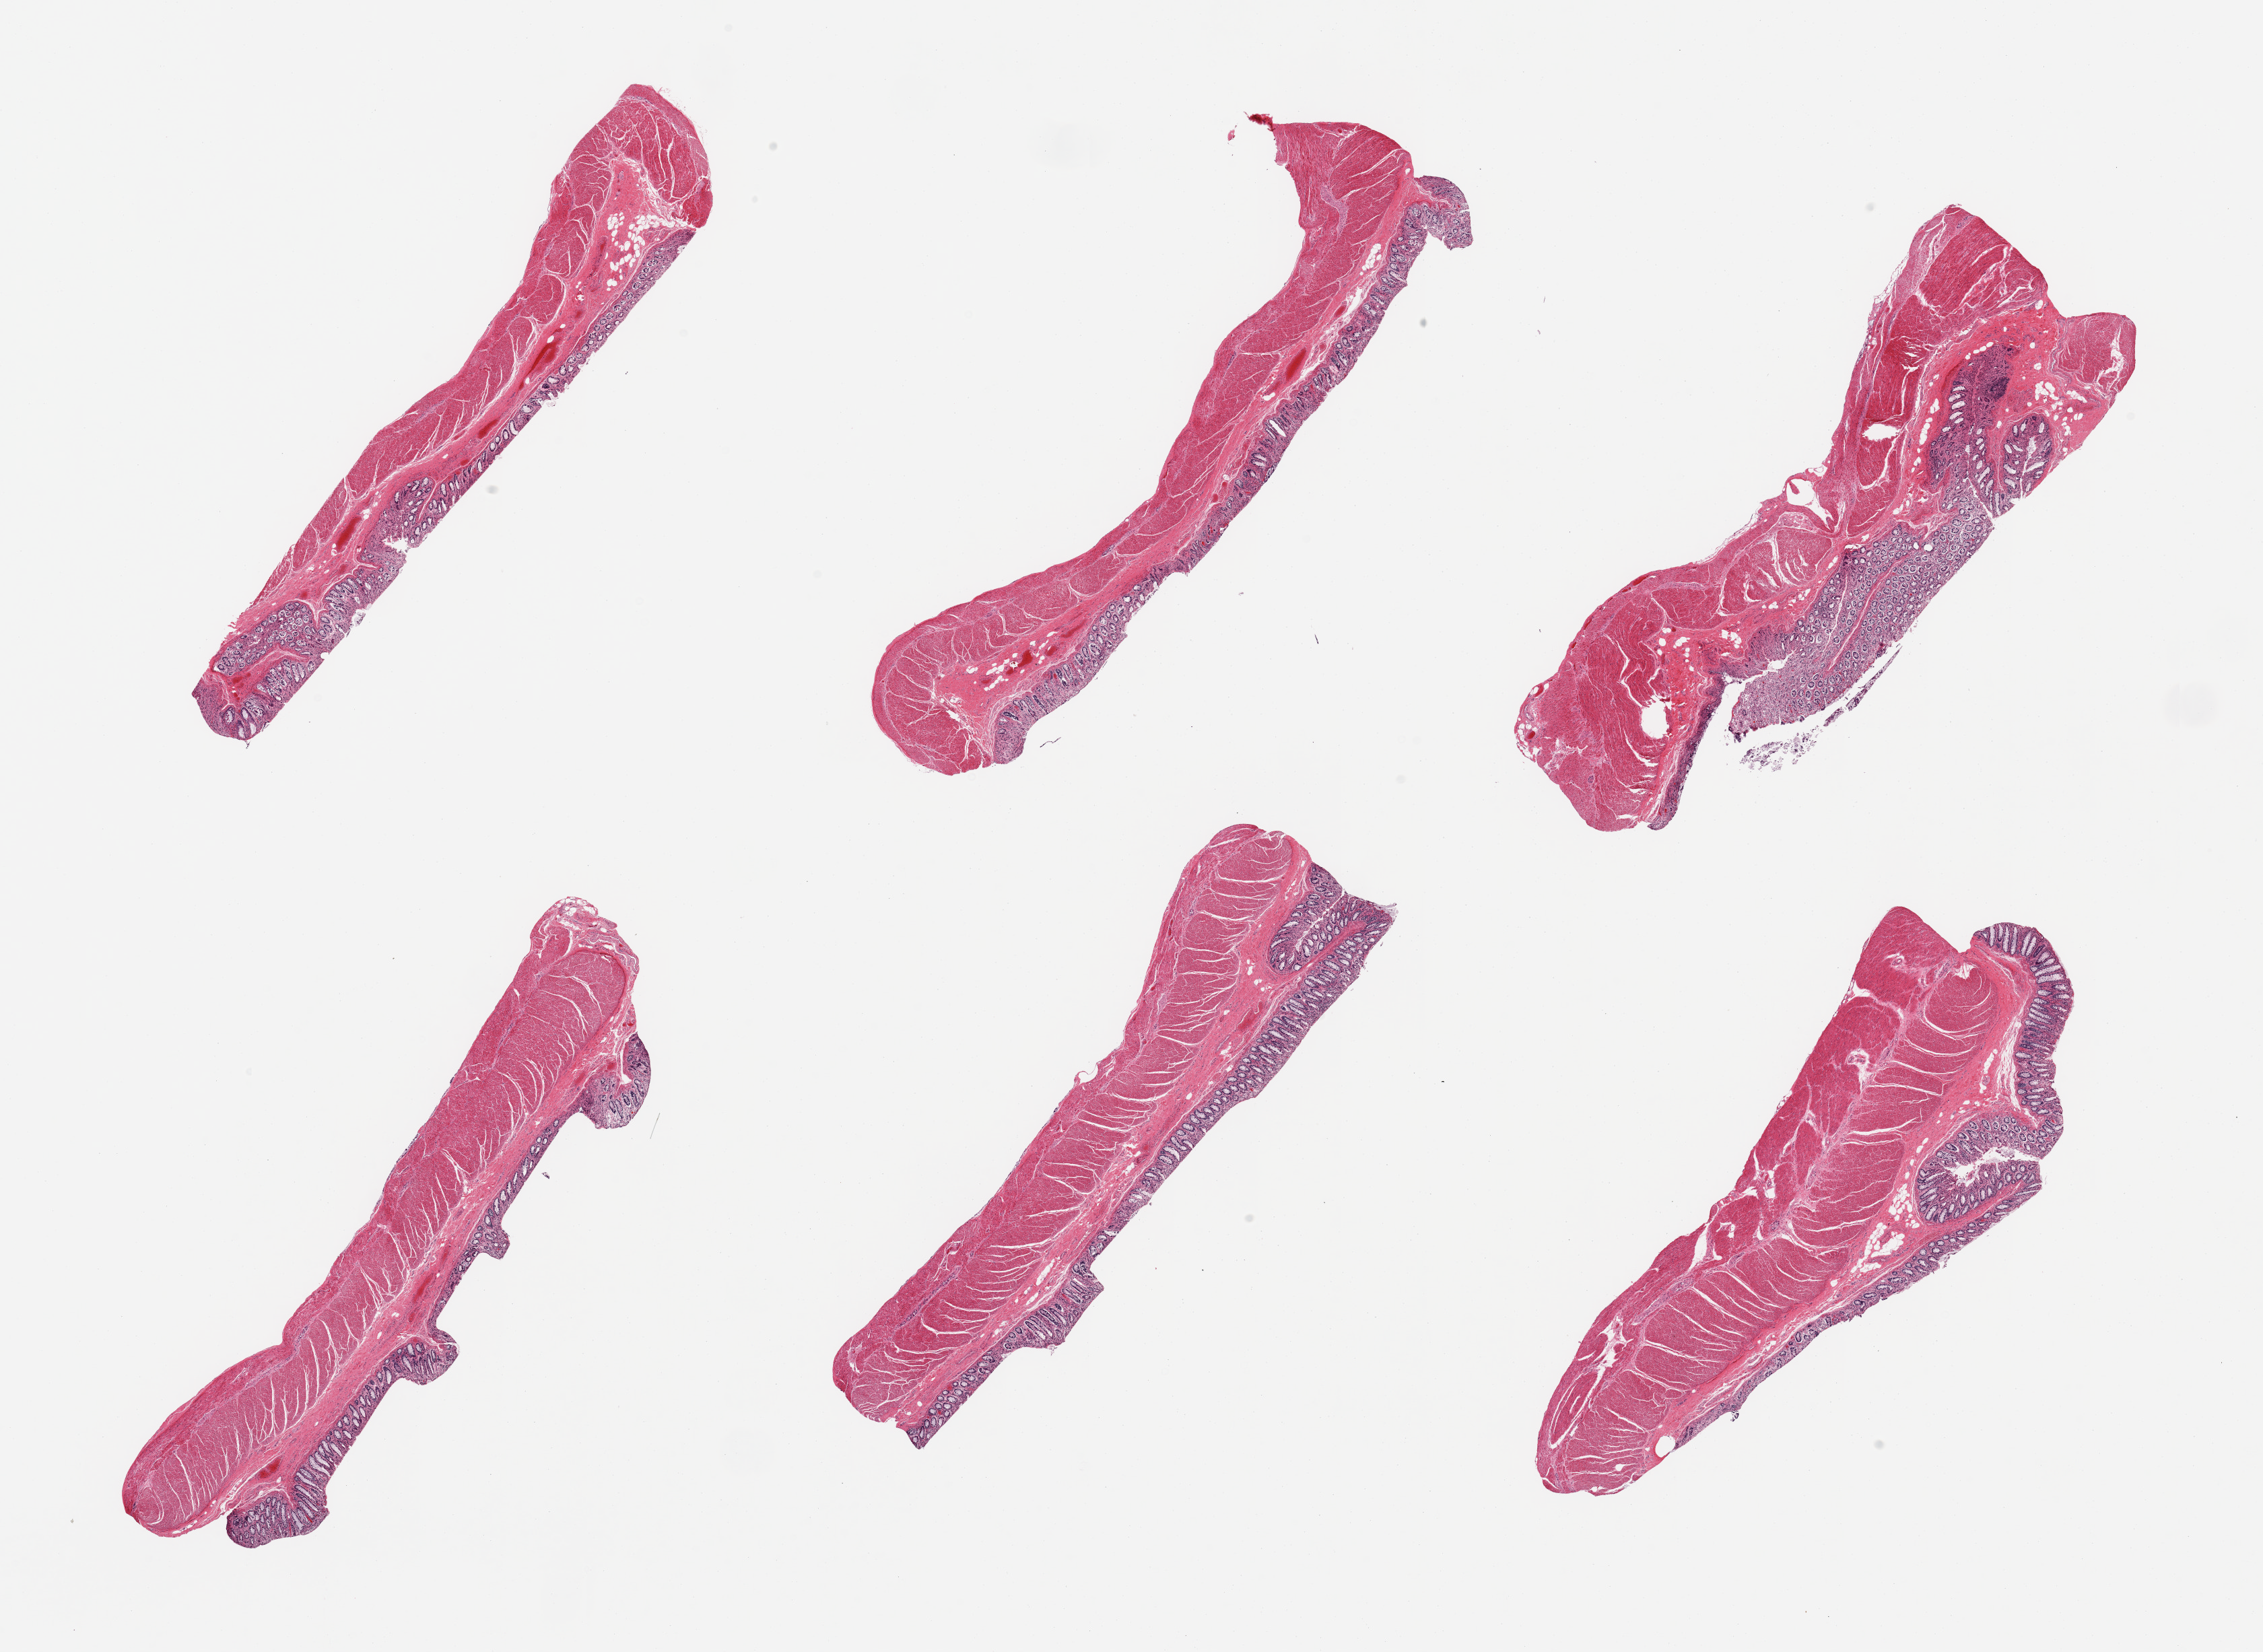
Digitized hematoxylin and eosin (H&E)-stained section, brightfield — whole scanned area (about 26.6 x 19.4 mm, from a 20x scan) shown as a low-resolution overview. PAXgene-fixed, paraffin-embedded tissue. Target tissue: transverse colon. Tissue donor sample. Donor: male.
Reviewer comment on this tissue sample: 6 pieces; well dissected.